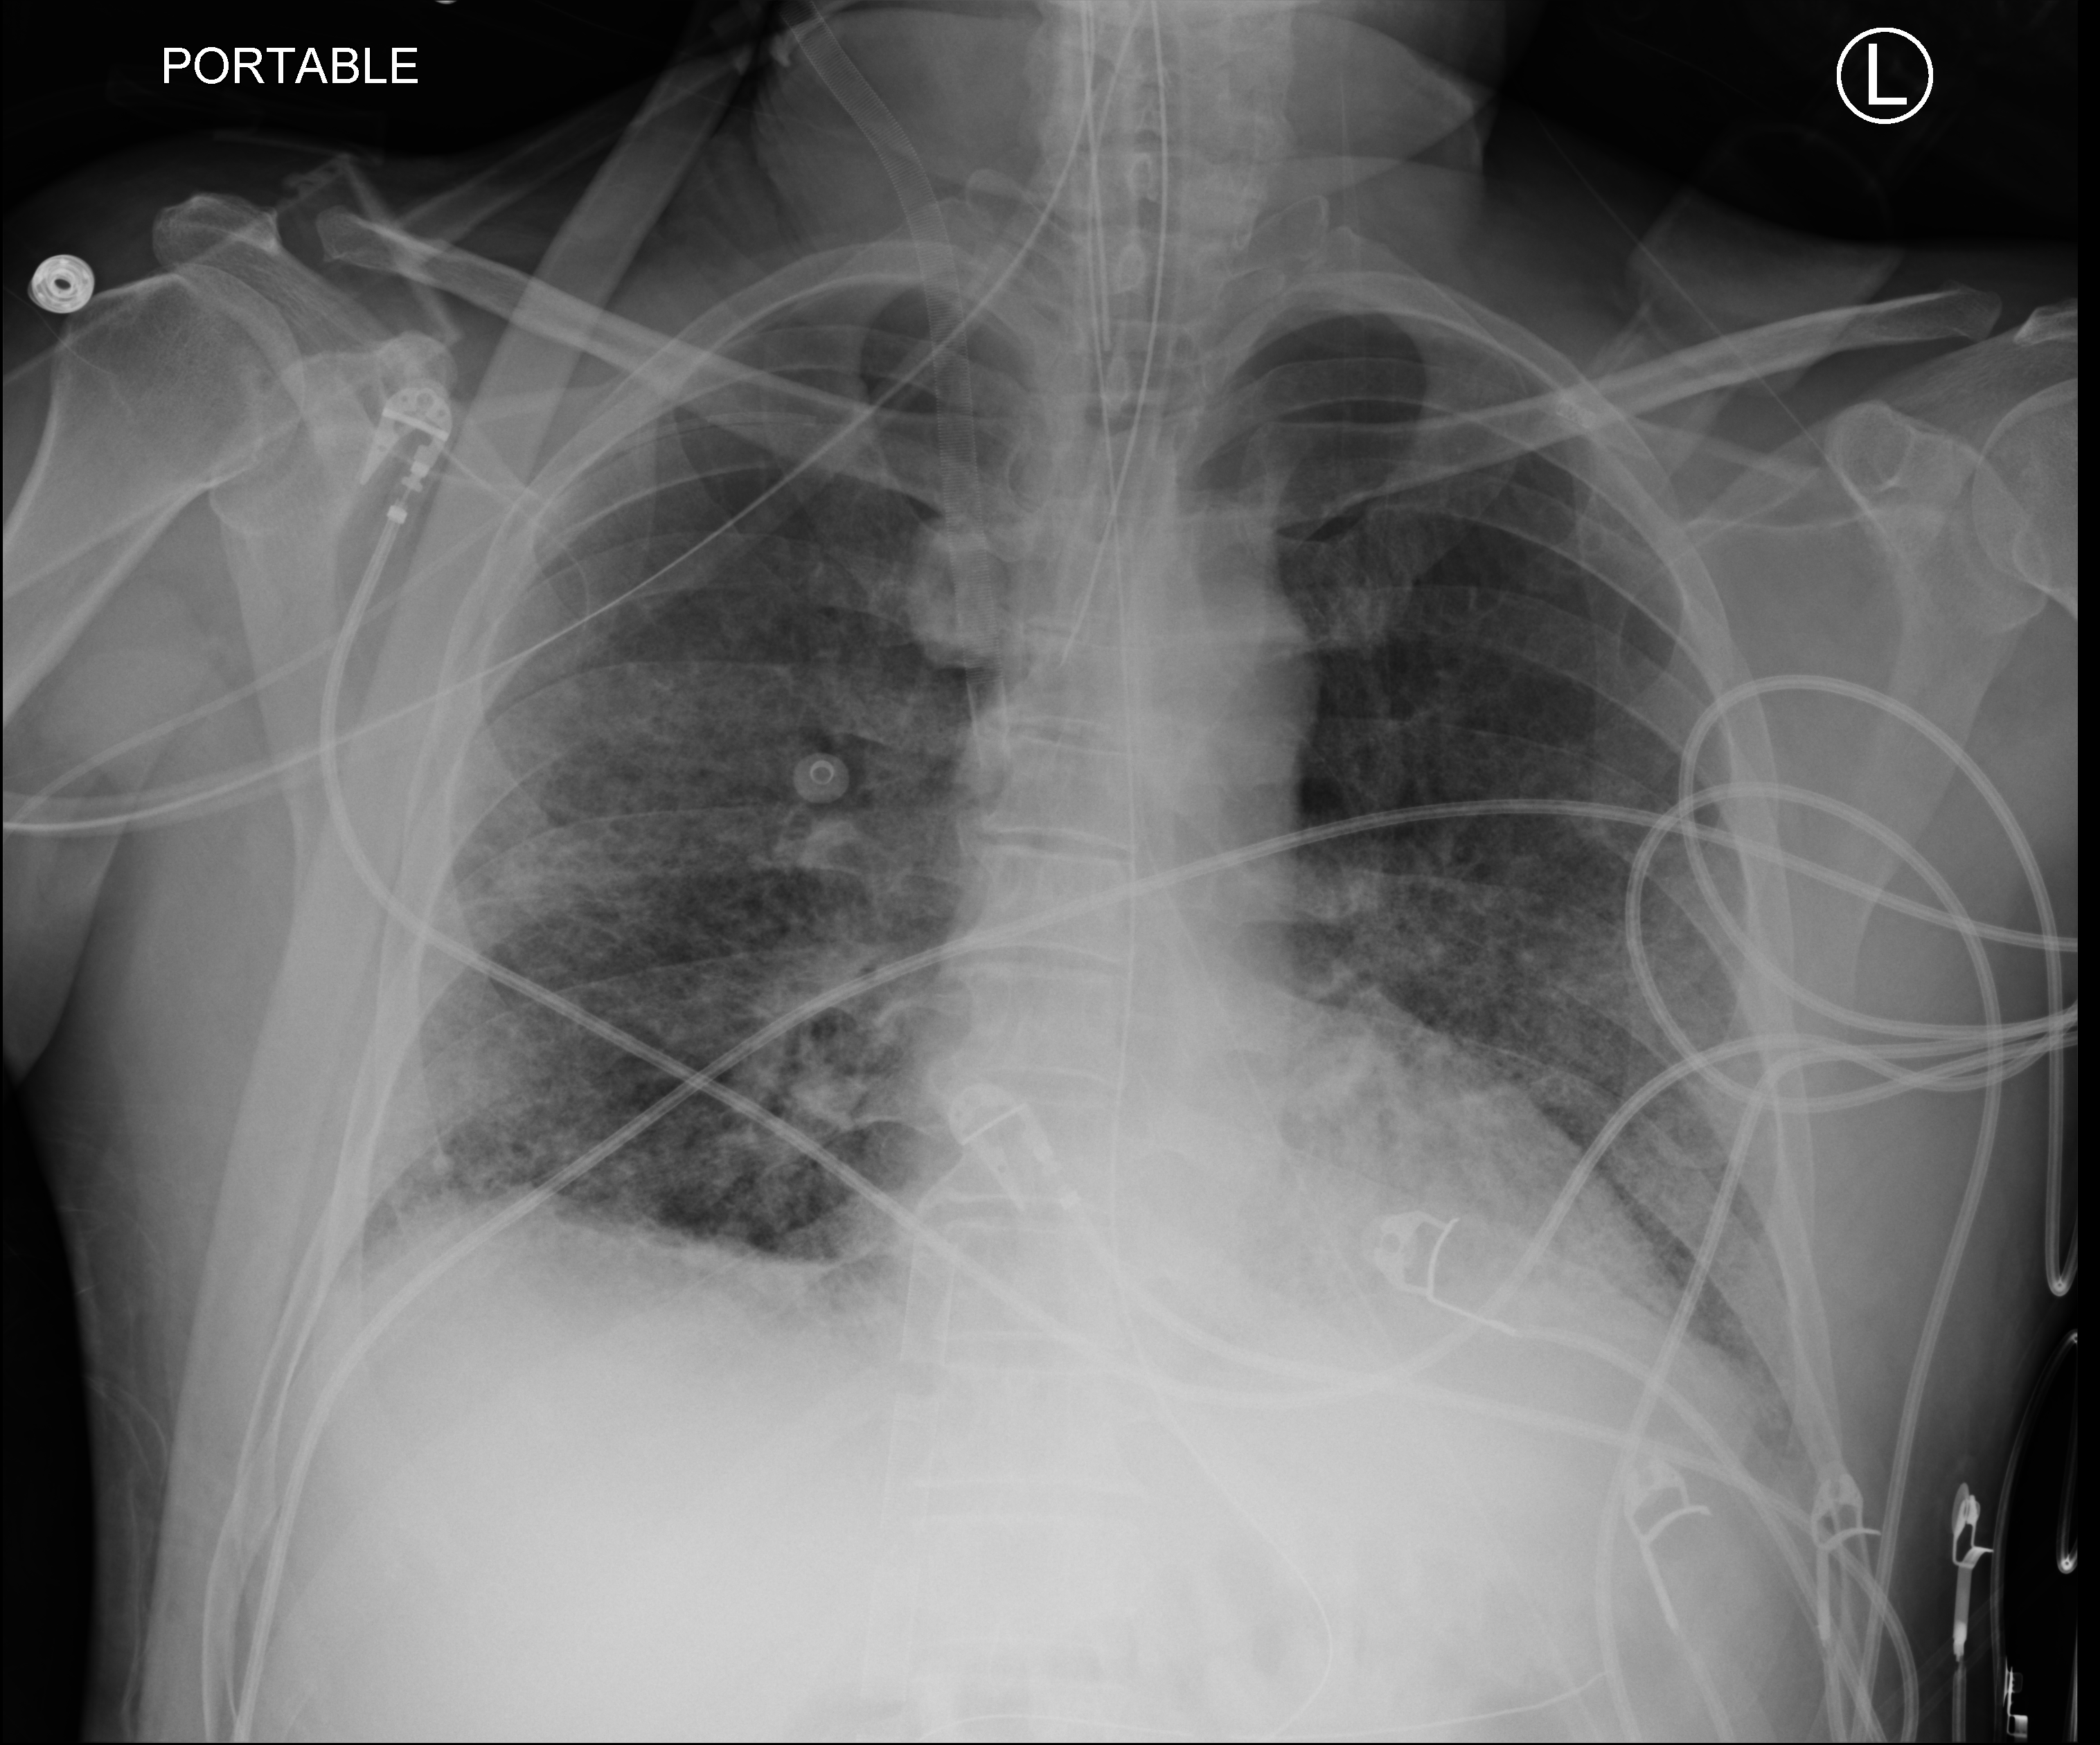
Portable chest radiograph, anteroposterior (AP) projection. Patient hospitalised with COVID-19; male, aged 18–59 years.
Admission-level facts for this patient (not findings on this image; timing relative to this image not recorded): diabetes (admission record): no; mechanically ventilated during this hospital stay: yes.